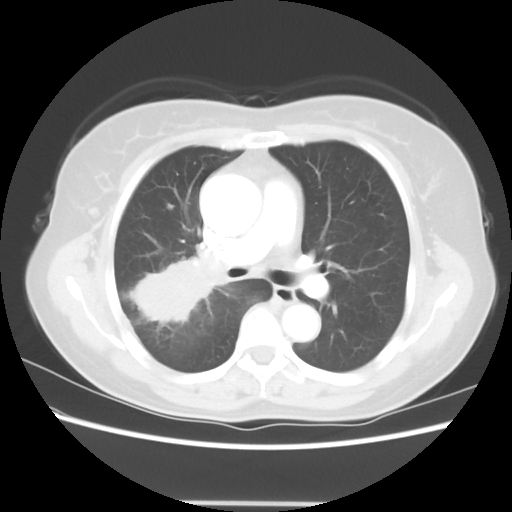
Chest CT, one axial slice. Slice 36 of 56 in the series (ordered by position). Reconstruction kernel STANDARD. Lung window (W 1500 / L -600 HU). 5 mm slice thickness. 512 × 512 image matrix, field of view 360 × 360 mm. Patient: female, 55 years. From the clinical record (not read from this slice): clinical TNM (as recorded): T2 N1 M0; histopathological grade: G2-3.
Structures marked on this image (rectangle marked by the reading radiologist):
- lung tumour (recorded histology: adenocarcinoma): bounding box (x1, y1, x2, y2) in pixels: (128, 256, 228, 330)